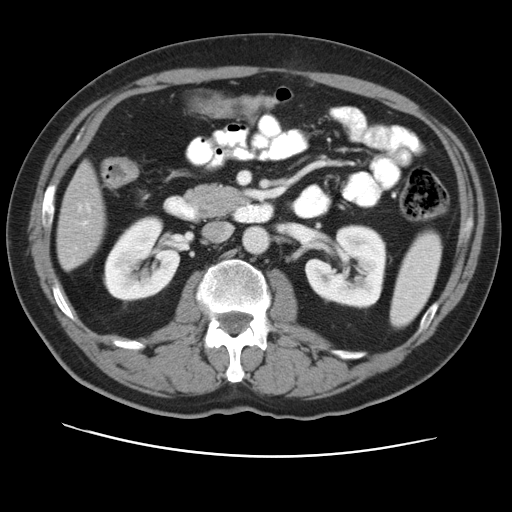
Contrast-enhanced abdominal CT, one axial slice; slice 17 of 49 in the series (ordered by position); reconstruction kernel STANDARD; 120 kVp; soft-tissue window (W 400 / L 40 HU); 5 mm slice thickness; 512 × 512 image matrix, field of view 374 × 374 mm. Male patient, age 59 years. Case-level facts recorded for this patient, not image findings: diagnosis: colorectal cancer liver metastases, imaged before liver resection; multiple liver metastases: yes; largest metastasis: 6.3 cm.
Annotated regions visible in this slice (outlined manually by an expert reader):
- liver: bounding box (x1, y1, x2, y2) in pixels: (58, 166, 105, 267)
- planned liver remnant (the part of the liver to remain after resection): (64, 166, 104, 229)
- portal vein (with intrahepatic branches): (84, 206, 89, 224)